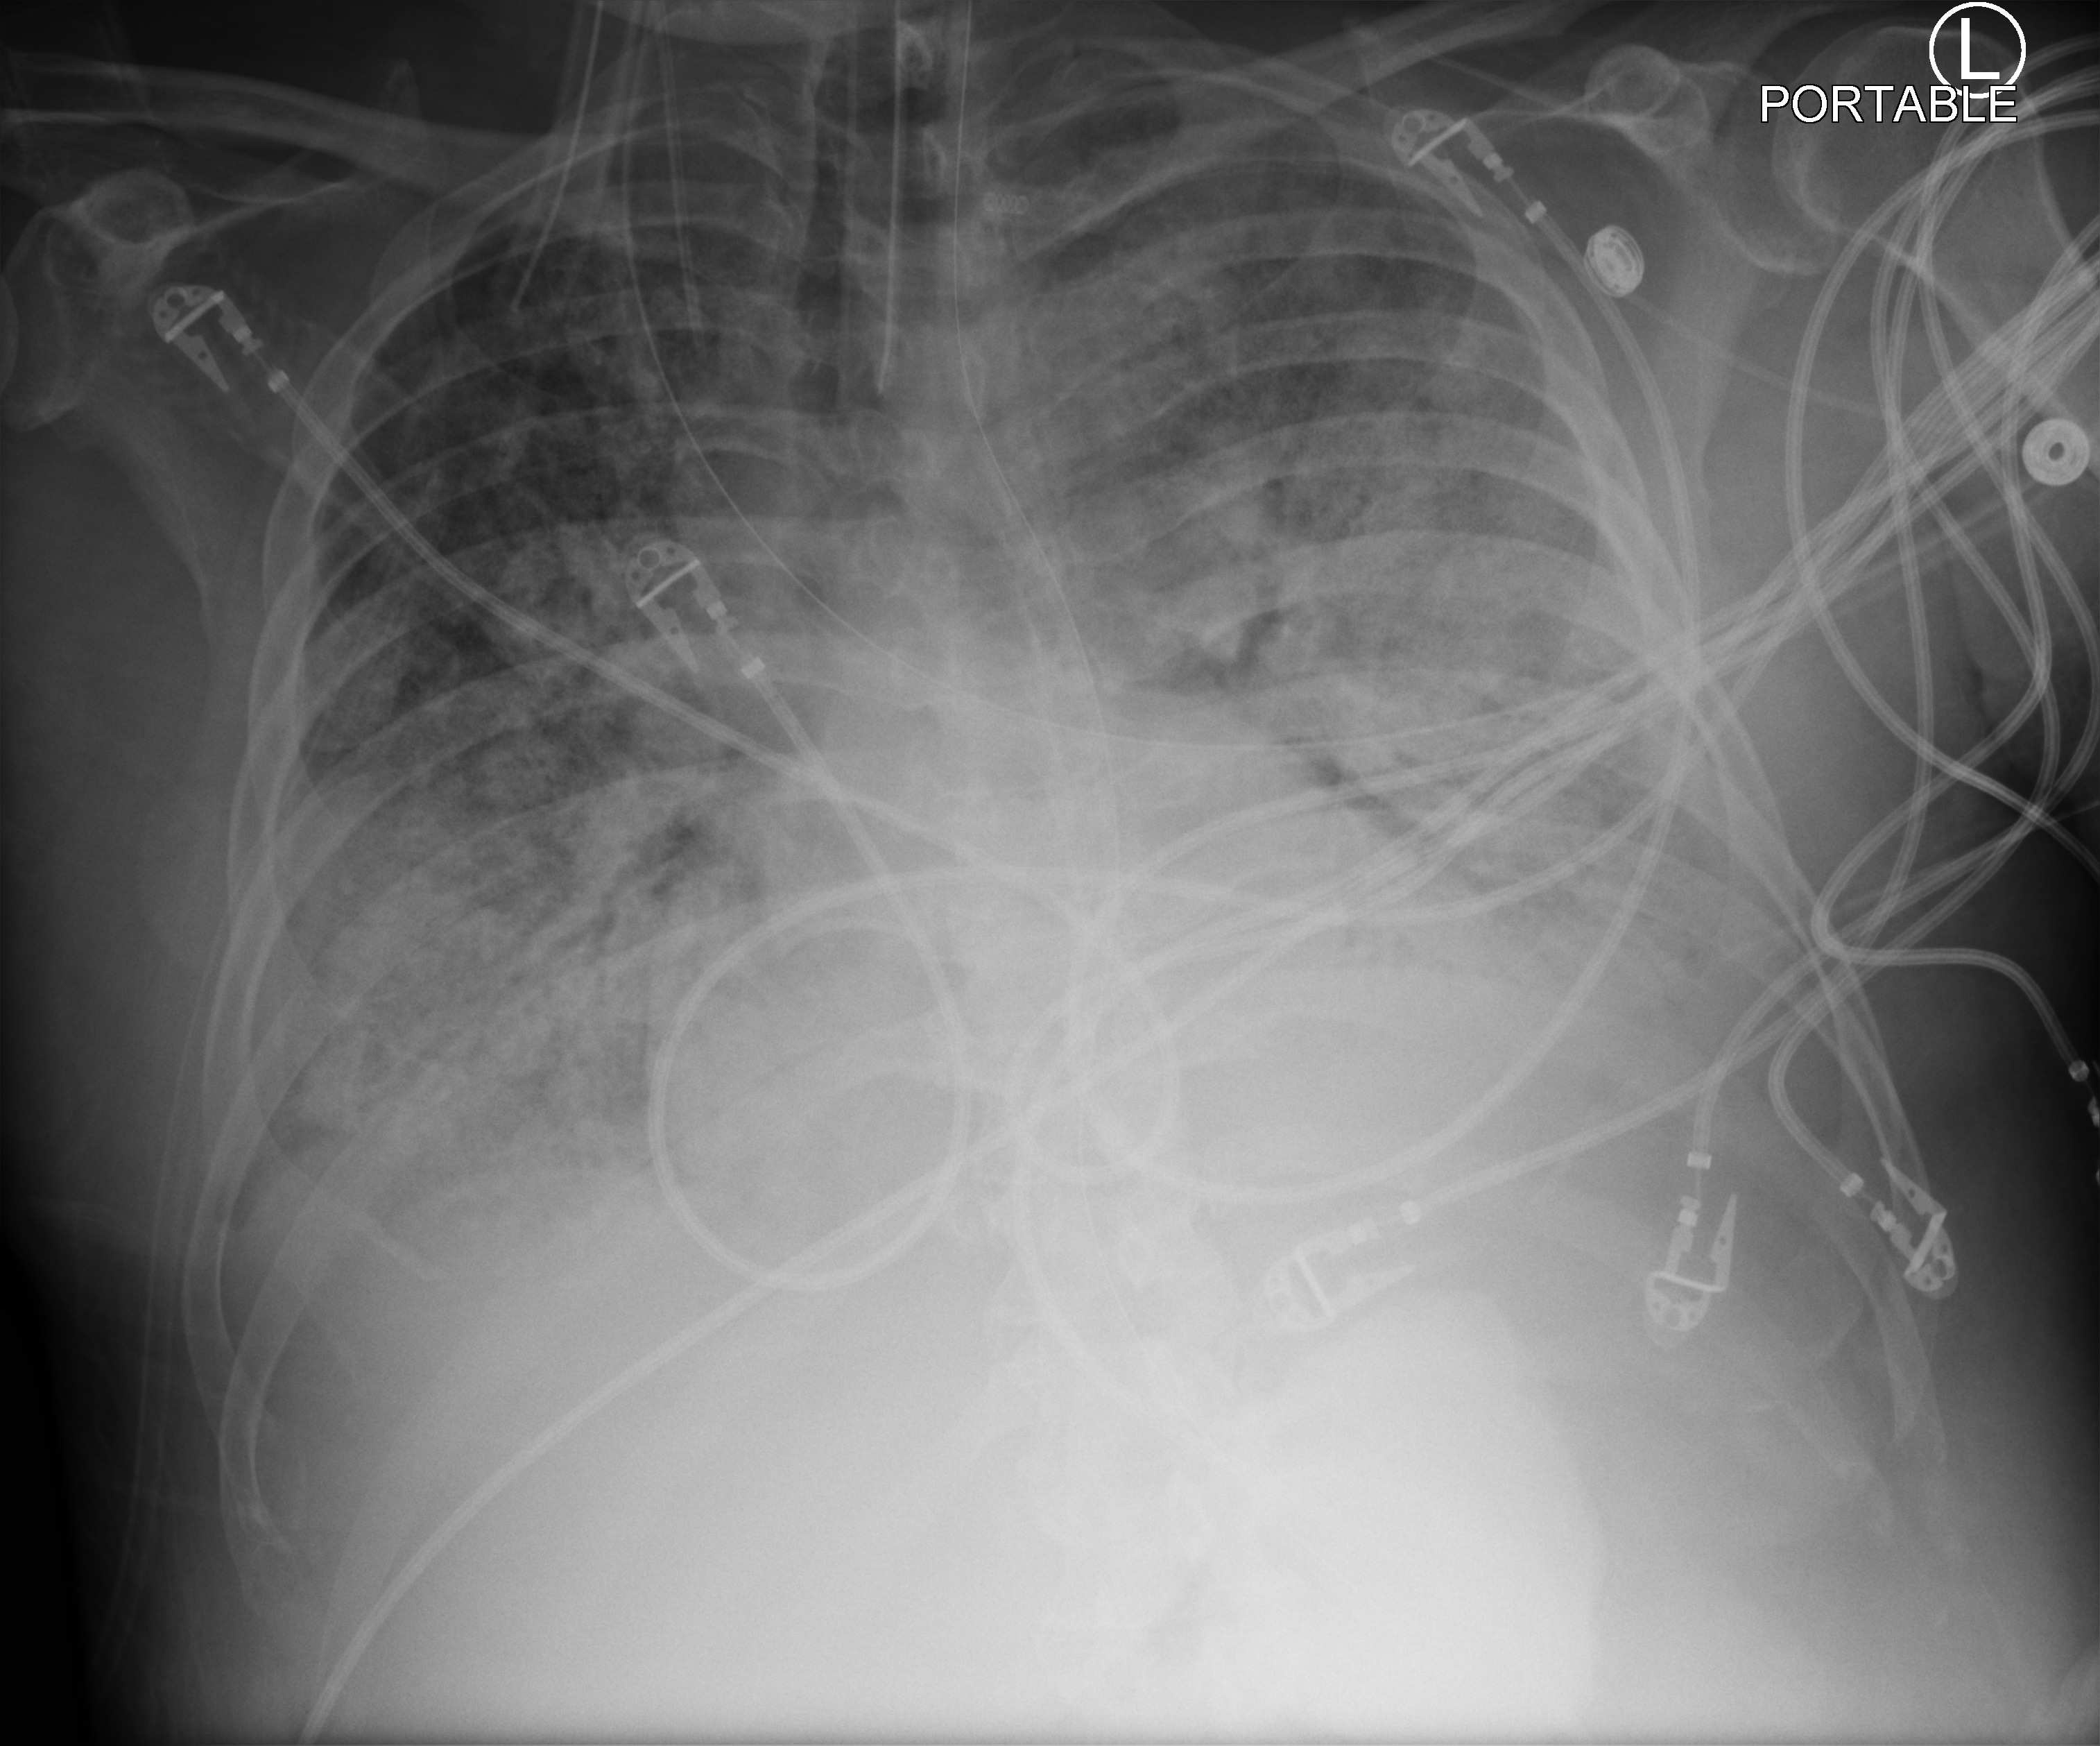
Portable chest radiograph; anteroposterior (AP) projection. Male patient hospitalised with COVID-19, age 60–74 years.
Hospital-stay facts (about this admission, not read from this image; timing relative to this image not recorded):
- admitted to intensive care during this hospital stay: yes